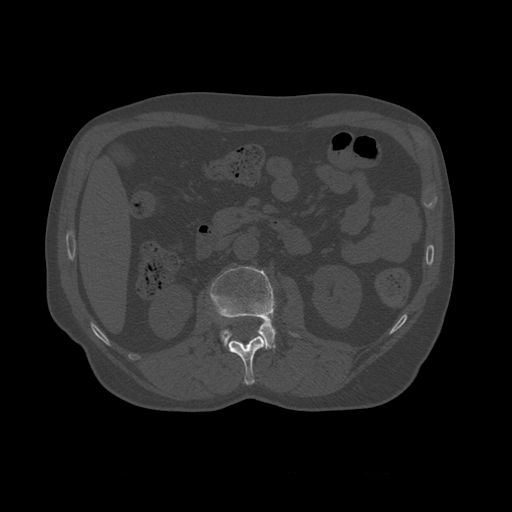
CT including the spine, one axial slice. Slice 343 of 450 in the series (ordered by position). 120 kVp. Bone window (W 1800 / L 400 HU). 1.25 mm slice thickness. 512 × 512 image matrix, field of view 405 × 405 mm. Patient age 75 years. From the clinical record (not read from this slice): primary cancer: prostate.
Annotated regions visible in this slice (semi-automatically segmented with operator editing):
- L1 vertebra: bounding box (x1, y1, x2, y2) in pixels: (228, 336, 266, 385)
- L2 vertebra: (210, 266, 299, 351)